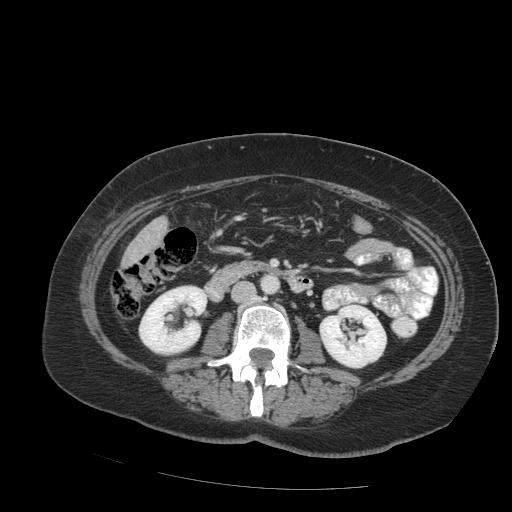
Contrast-enhanced abdominal CT (liver protocol), one axial slice. Position 22 of 99 along the scan axis. Reconstruction kernel STANDARD. 140 kVp. Soft-tissue window (W 400 / L 40 HU). 2.5 mm slice thickness. 512 × 512 image matrix, field of view 400 × 400 mm. Case-level facts recorded for this patient, not image findings: diagnosis: hepatocellular carcinoma (patient treated with transarterial chemoembolisation; whether this scan precedes or follows treatment is not stated here); TNM stage (as recorded): Stage-IVB; Child-Pugh class: A; tumour differentiation: moderately differentiated; tumour nodularity: uninodular.
Structures marked on this image (semi-automatic segmentation, software-assisted and operator-edited):
- liver parenchyma outside the tumour (the mass and vessels are separate outlines, so this box may not span the whole liver): box from (x=122, y=216) to (x=168, y=266) px